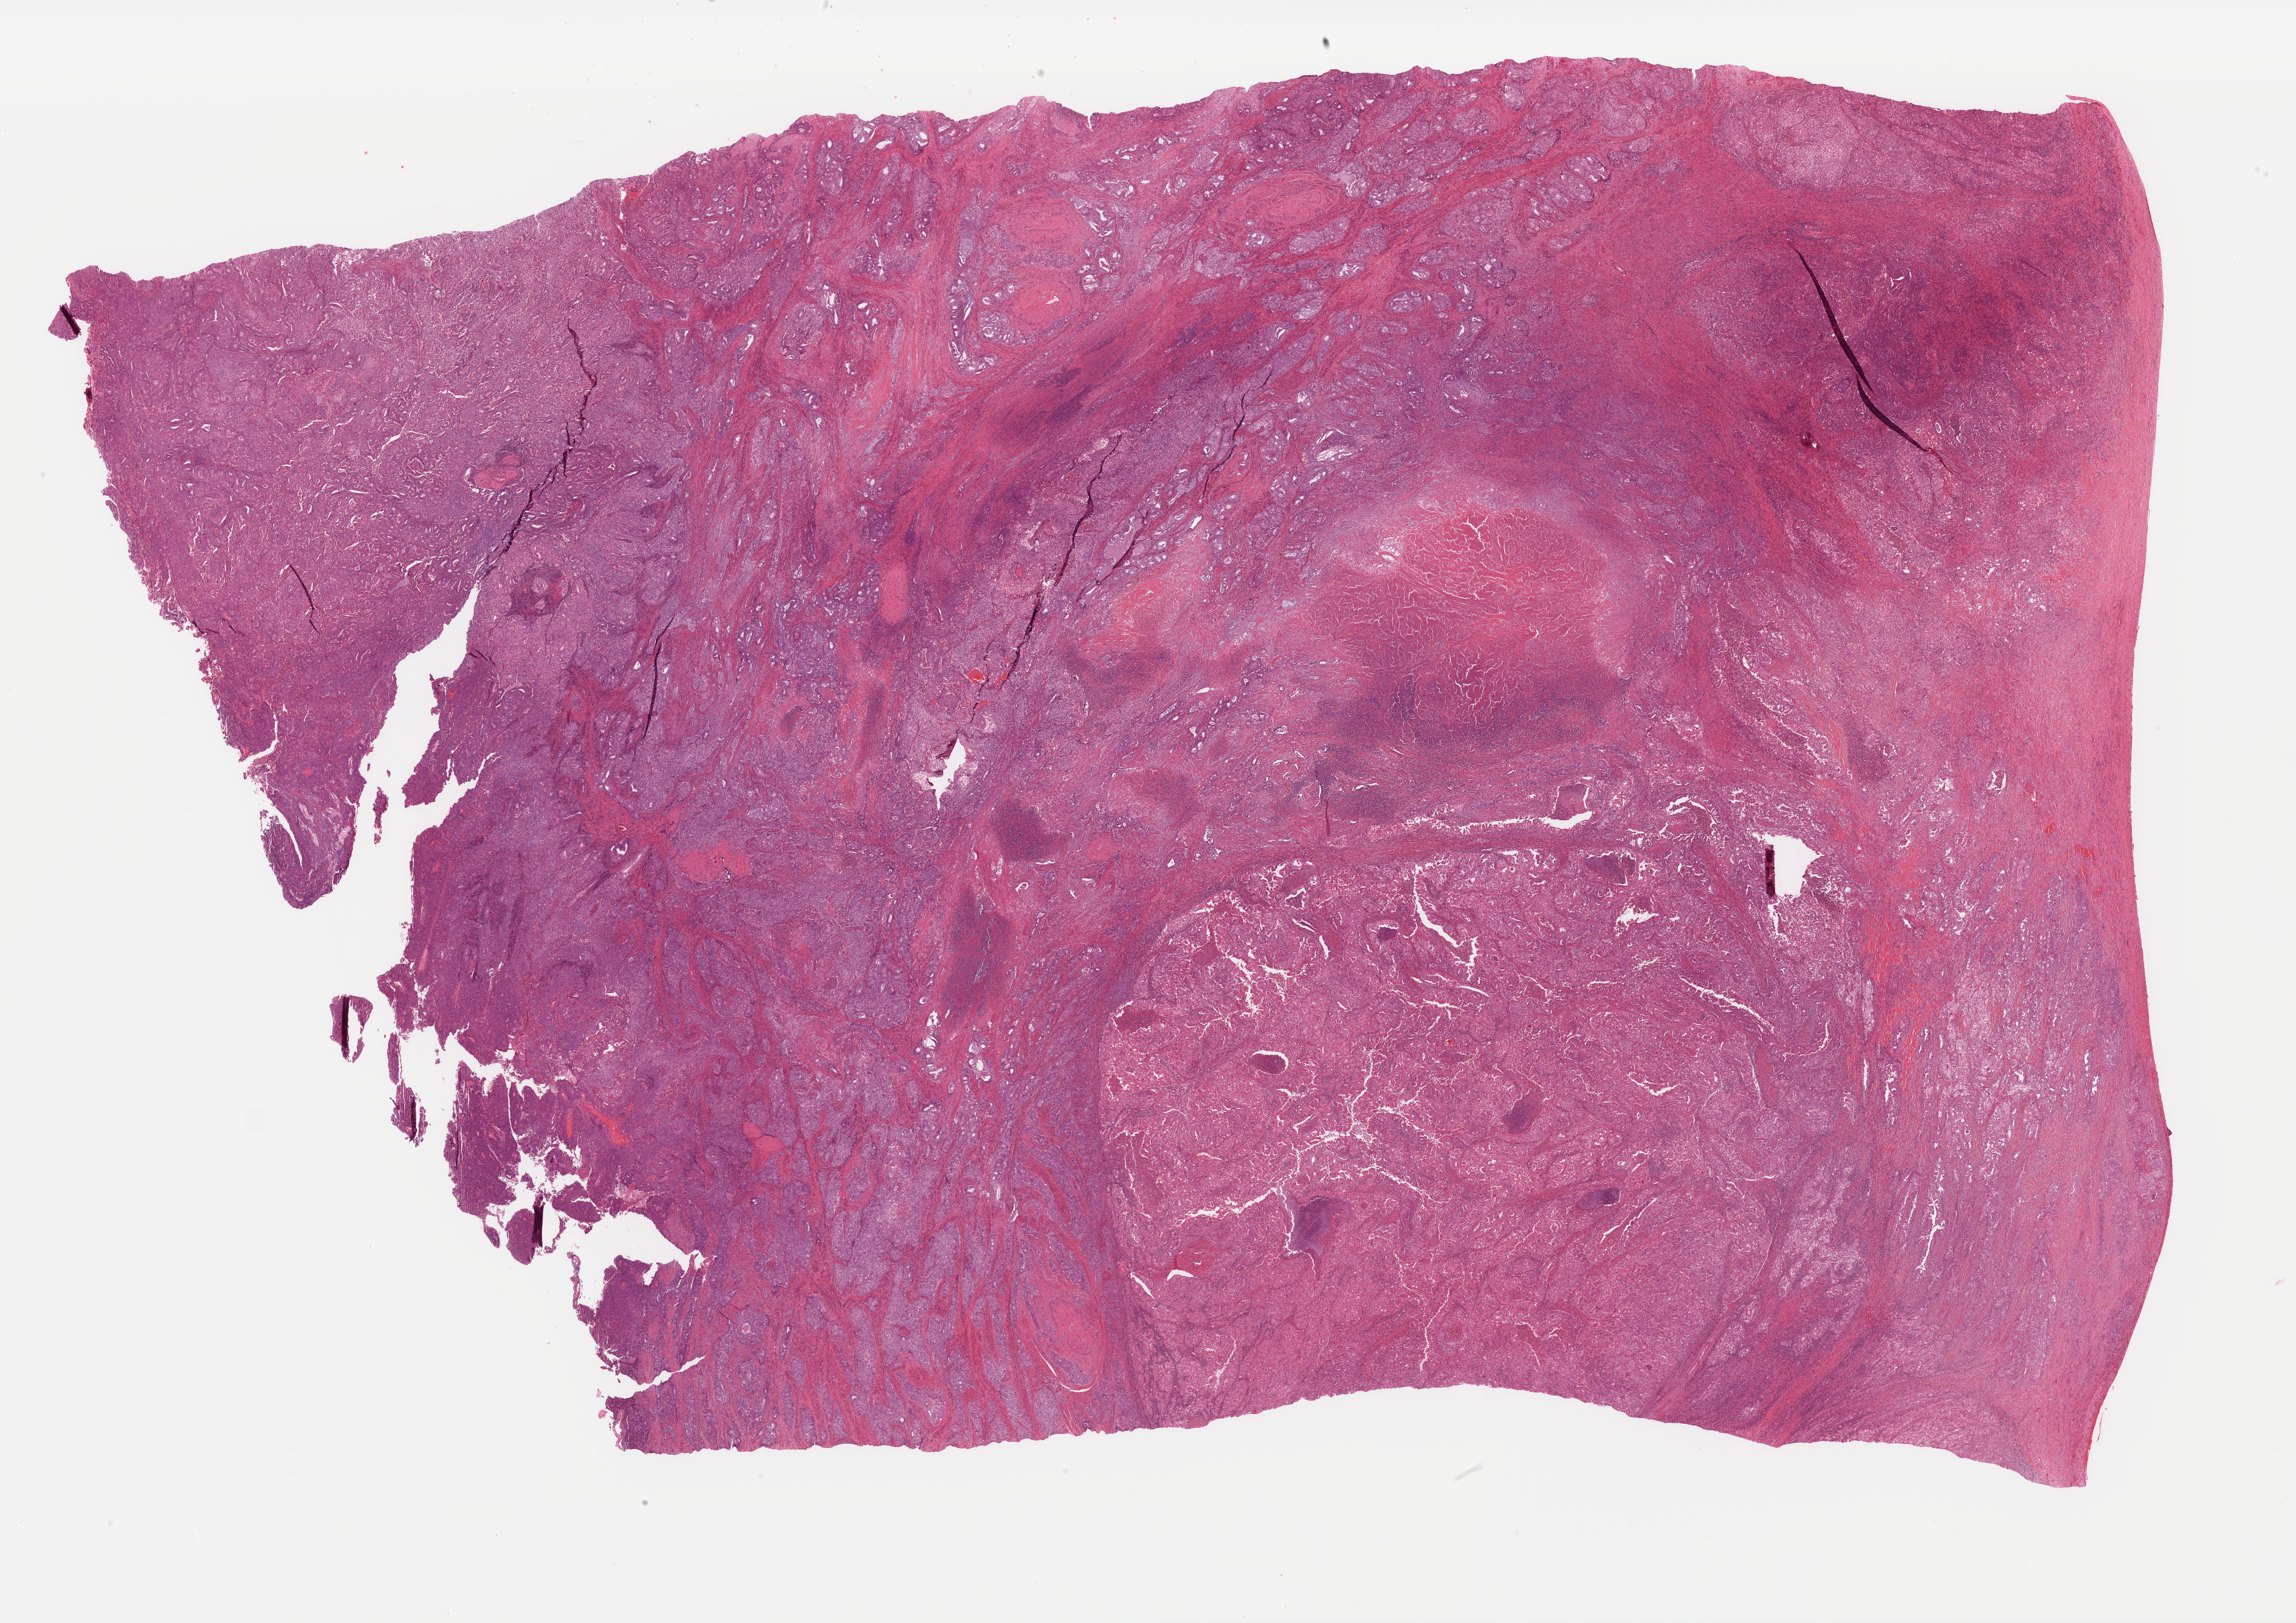
H&E whole-slide image — a low-resolution overview of the entire scanned area, about 29.8 x 21.1 mm. Formalin-fixed paraffin-embedded (FFPE) diagnostic section. Primary tumour sample from the uterus. Female, age 81 years at initial diagnosis. Histologic grade: G3 (poorly differentiated).
FIGO stage: IIIC. Pathologic diagnosis: Endometrioid adenocarcinoma, NOS (endometrium).